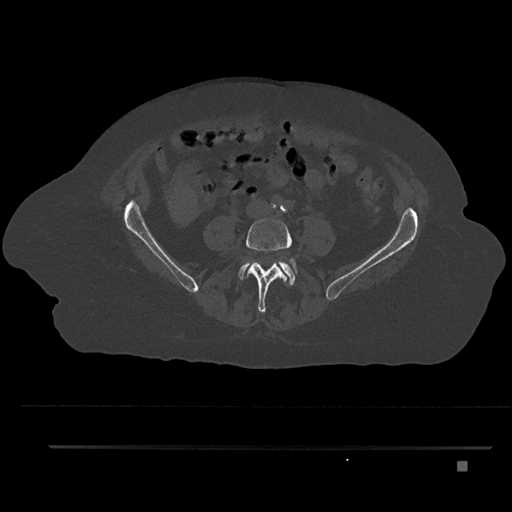
CT including the spine, one axial slice; position 72 of 797 along the scan axis; 120 kVp; bone window (W 1800 / L 400 HU); 0.5 mm slice thickness; 512 × 512 image matrix, field of view 437 × 437 mm. Patient: female, 76 years. Case-level facts recorded for this patient, not image findings: primary cancer: lung.
Outlined on this slice (semi-automatically segmented with operator editing):
- L4 vertebra: bounding box [x1, y1, x2, y2] px = [245, 218, 298, 313]
- L5 vertebra: [238, 259, 296, 286]